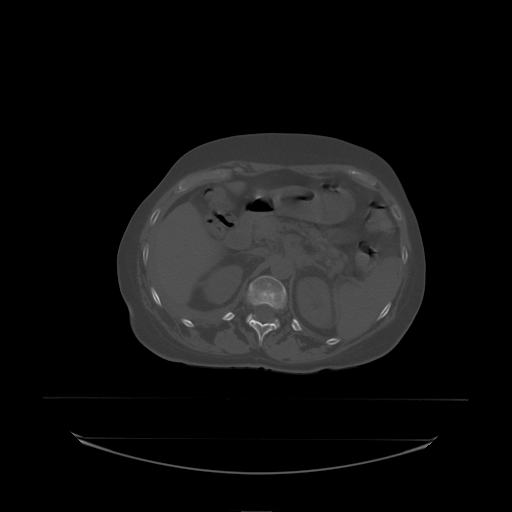
CT including the spine, one axial slice. Bone window (W 1800 / L 400 HU). 2.5 mm slice thickness. 512 × 512 image matrix, field of view 500 × 500 mm. Patient: female, 53 years. Case-level facts recorded for this patient, not image findings: primary cancer: lung.
Structures marked on this image (semi-automatically segmented with operator editing):
- L1 vertebra: bounding box (x1, y1, x2, y2) in pixels: (246, 276, 287, 328)
- T12 vertebra: (249, 319, 277, 338)